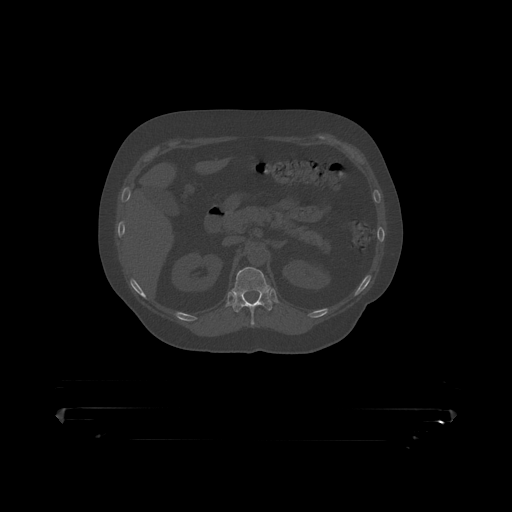
CT including the spine, one axial slice. Slice 175 of 390 in the series (ordered by position). Reconstruction kernel STANDARD. 120 kVp. Bone window (W 1800 / L 400 HU). 1.25 mm slice thickness. 512 × 512 image matrix, field of view 650 × 650 mm. Patient: male, 60 years. Case-level facts recorded for this patient, not image findings: primary cancer: prostate.
Annotated regions visible in this slice (semi-automatic segmentation, software-assisted and operator-edited):
- T12 vertebra: bounding box <232,267,273,319> (left, top, right, bottom; pixels)